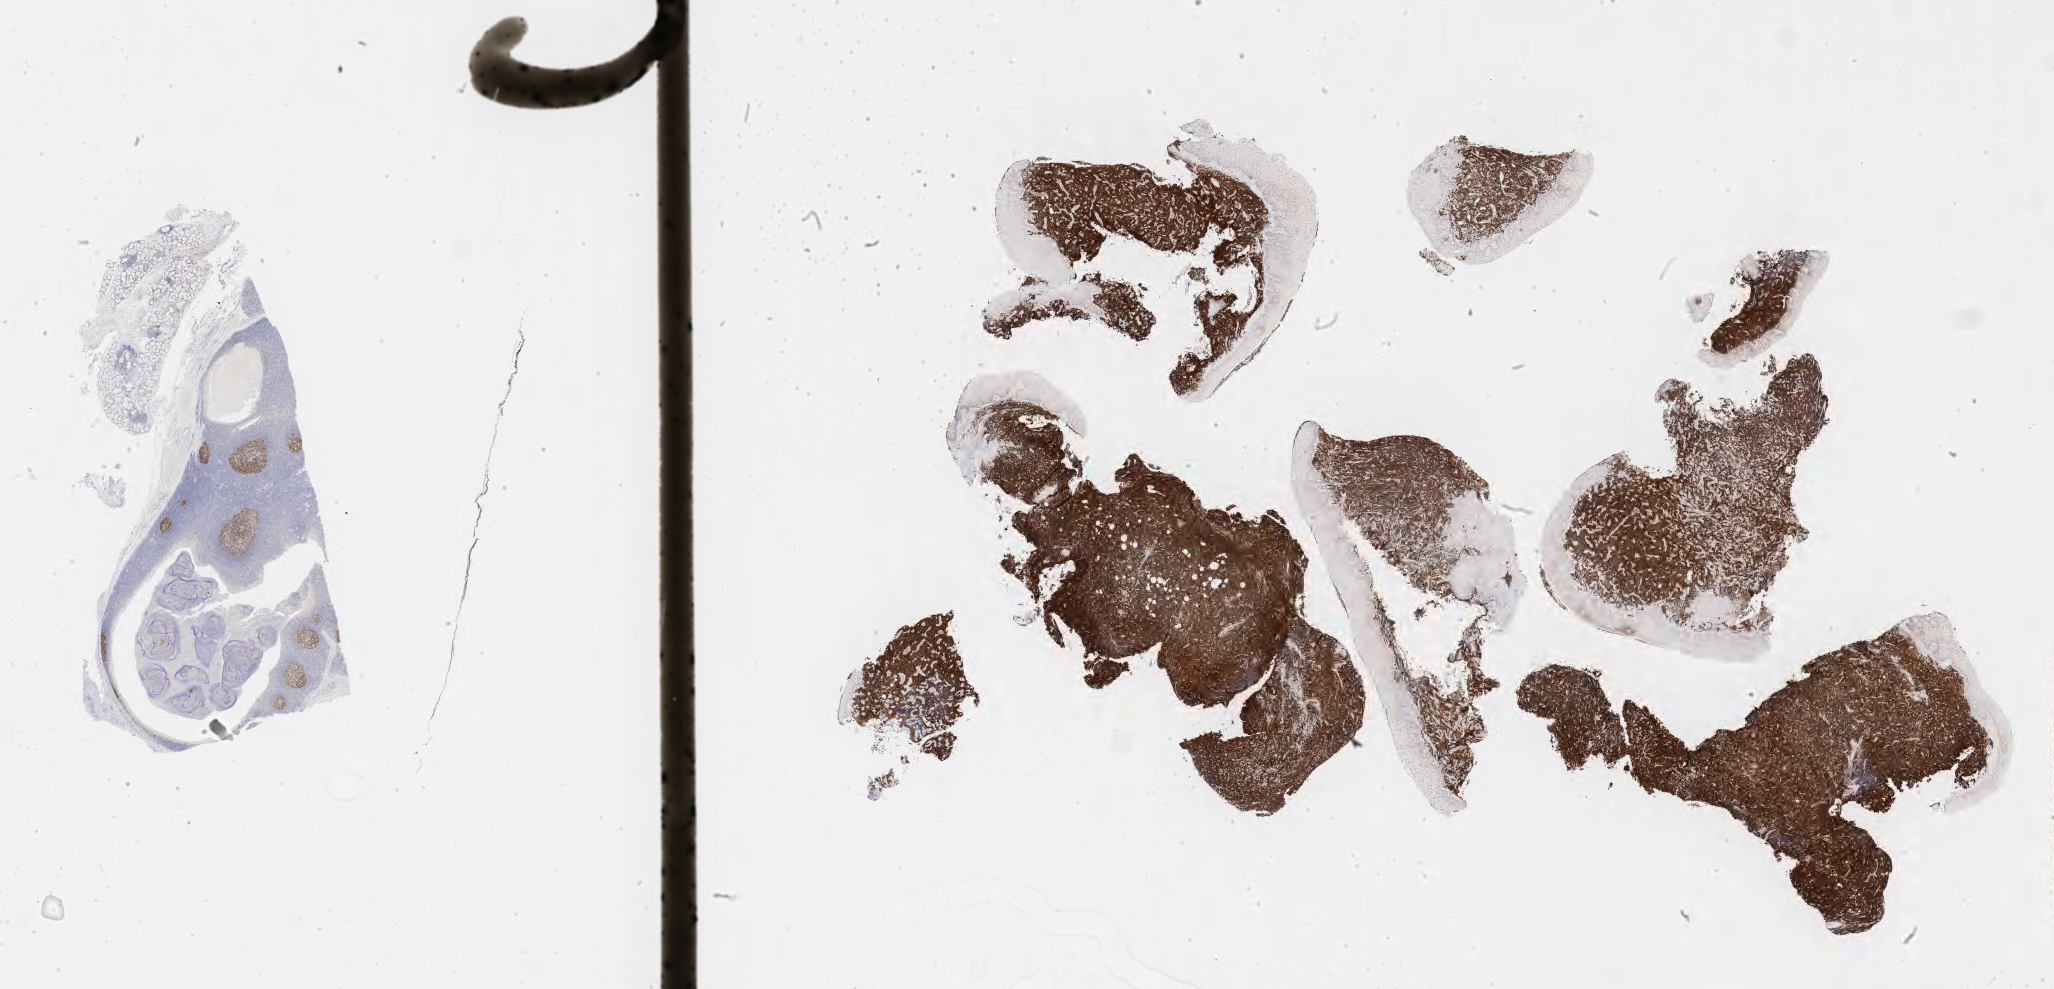
IHC for BCL6, whole-slide image — whole scanned area (about 33.2 x 16.0 mm) shown as a low-resolution overview, specimen: tumor tissue. Male patient, aged 43.
Diagnosis: Burkitt lymphoma, NOS.